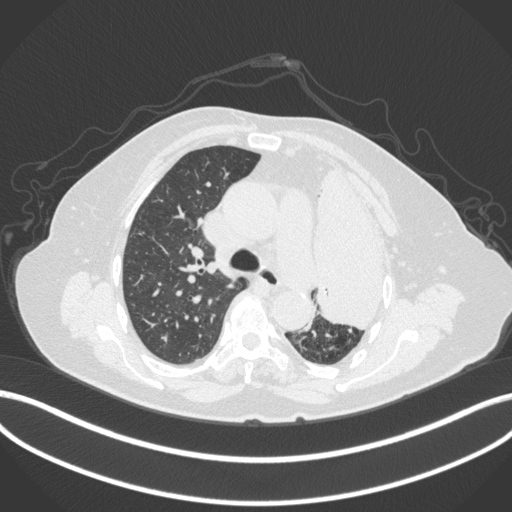
Chest CT, one axial slice. Position 264 of 399 along the scan axis. Reconstruction kernel B31f. Lung window (W 1500 / L -600 HU). 1 mm slice thickness. 512 × 512 image matrix, field of view 400 × 400 mm. Patient: female, 75 years. Case-level facts recorded for this patient, not image findings: clinical TNM (as recorded): T3 N3 M1.
Outlined on this slice (rectangle marked by the reading radiologist):
- lung tumour (recorded histology: adenocarcinoma): bounding box [x1, y1, x2, y2] px = [310, 161, 403, 334]